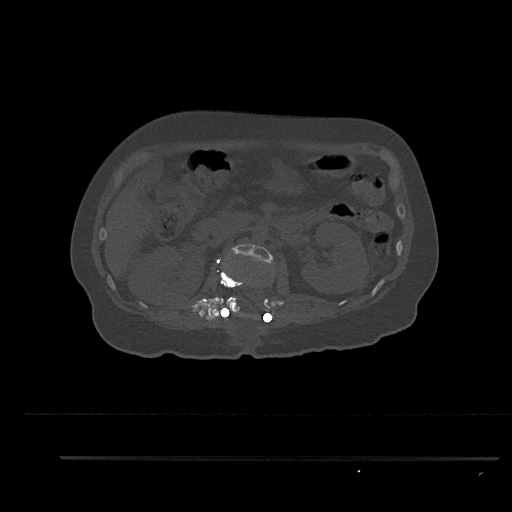
CT including the spine, one axial slice; slice 190 of 797 in the series (ordered by position); 120 kVp; bone window (W 1800 / L 400 HU); 512 × 512 image matrix, field of view 408 × 408 mm. Female patient, age 44 years. From the clinical record (not read from this slice): primary cancer: renal.
Outlined on this slice (semi-automatic segmentation, software-assisted and operator-edited):
- L1 vertebra: bounding box <217,262,243,317> (left, top, right, bottom; pixels)
- L2 vertebra: <226,244,272,314>